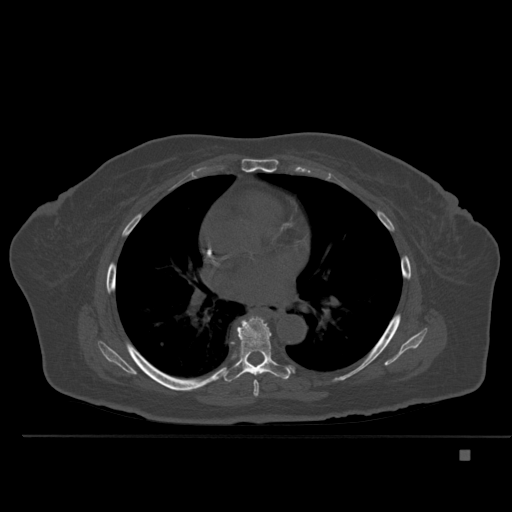
CT including the spine, one axial slice; slice 328 of 477 in the series (ordered by position); bone window (W 1800 / L 400 HU); 1.5 mm slice thickness; 512 × 512 image matrix. Patient: female, 74 years. From the clinical record (not read from this slice): primary cancer: colon.
Outlined on this slice (semi-automatic segmentation, software-assisted and operator-edited):
- T6 vertebra: bounding box <253,380,259,397> (left, top, right, bottom; pixels)
- T7 vertebra: <223,317,293,382>